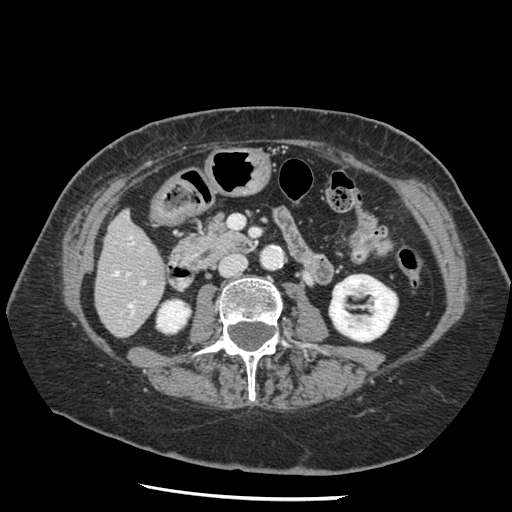
Contrast-enhanced abdominal CT, one axial slice; slice 42 of 148 in the series (ordered by position); reconstruction kernel STANDARD; 120 kVp; intravenous contrast given; soft-tissue window (W 400 / L 40 HU); 512 × 512 image matrix, field of view 330 × 330 mm. Female patient, age 85 years. From the clinical record (not read from this slice): diagnosis: colorectal cancer liver metastases, imaged before liver resection; multiple liver metastases: no; largest metastasis: 0.9 cm; disease in both lobes: no.
Structures marked on this image (outlined manually by an expert reader):
- hepatic veins: bounding box <115,271,132,308> (left, top, right, bottom; pixels)
- liver: <96,213,166,337>
- planned liver remnant (the part of the liver to remain after resection): <96,213,166,333>